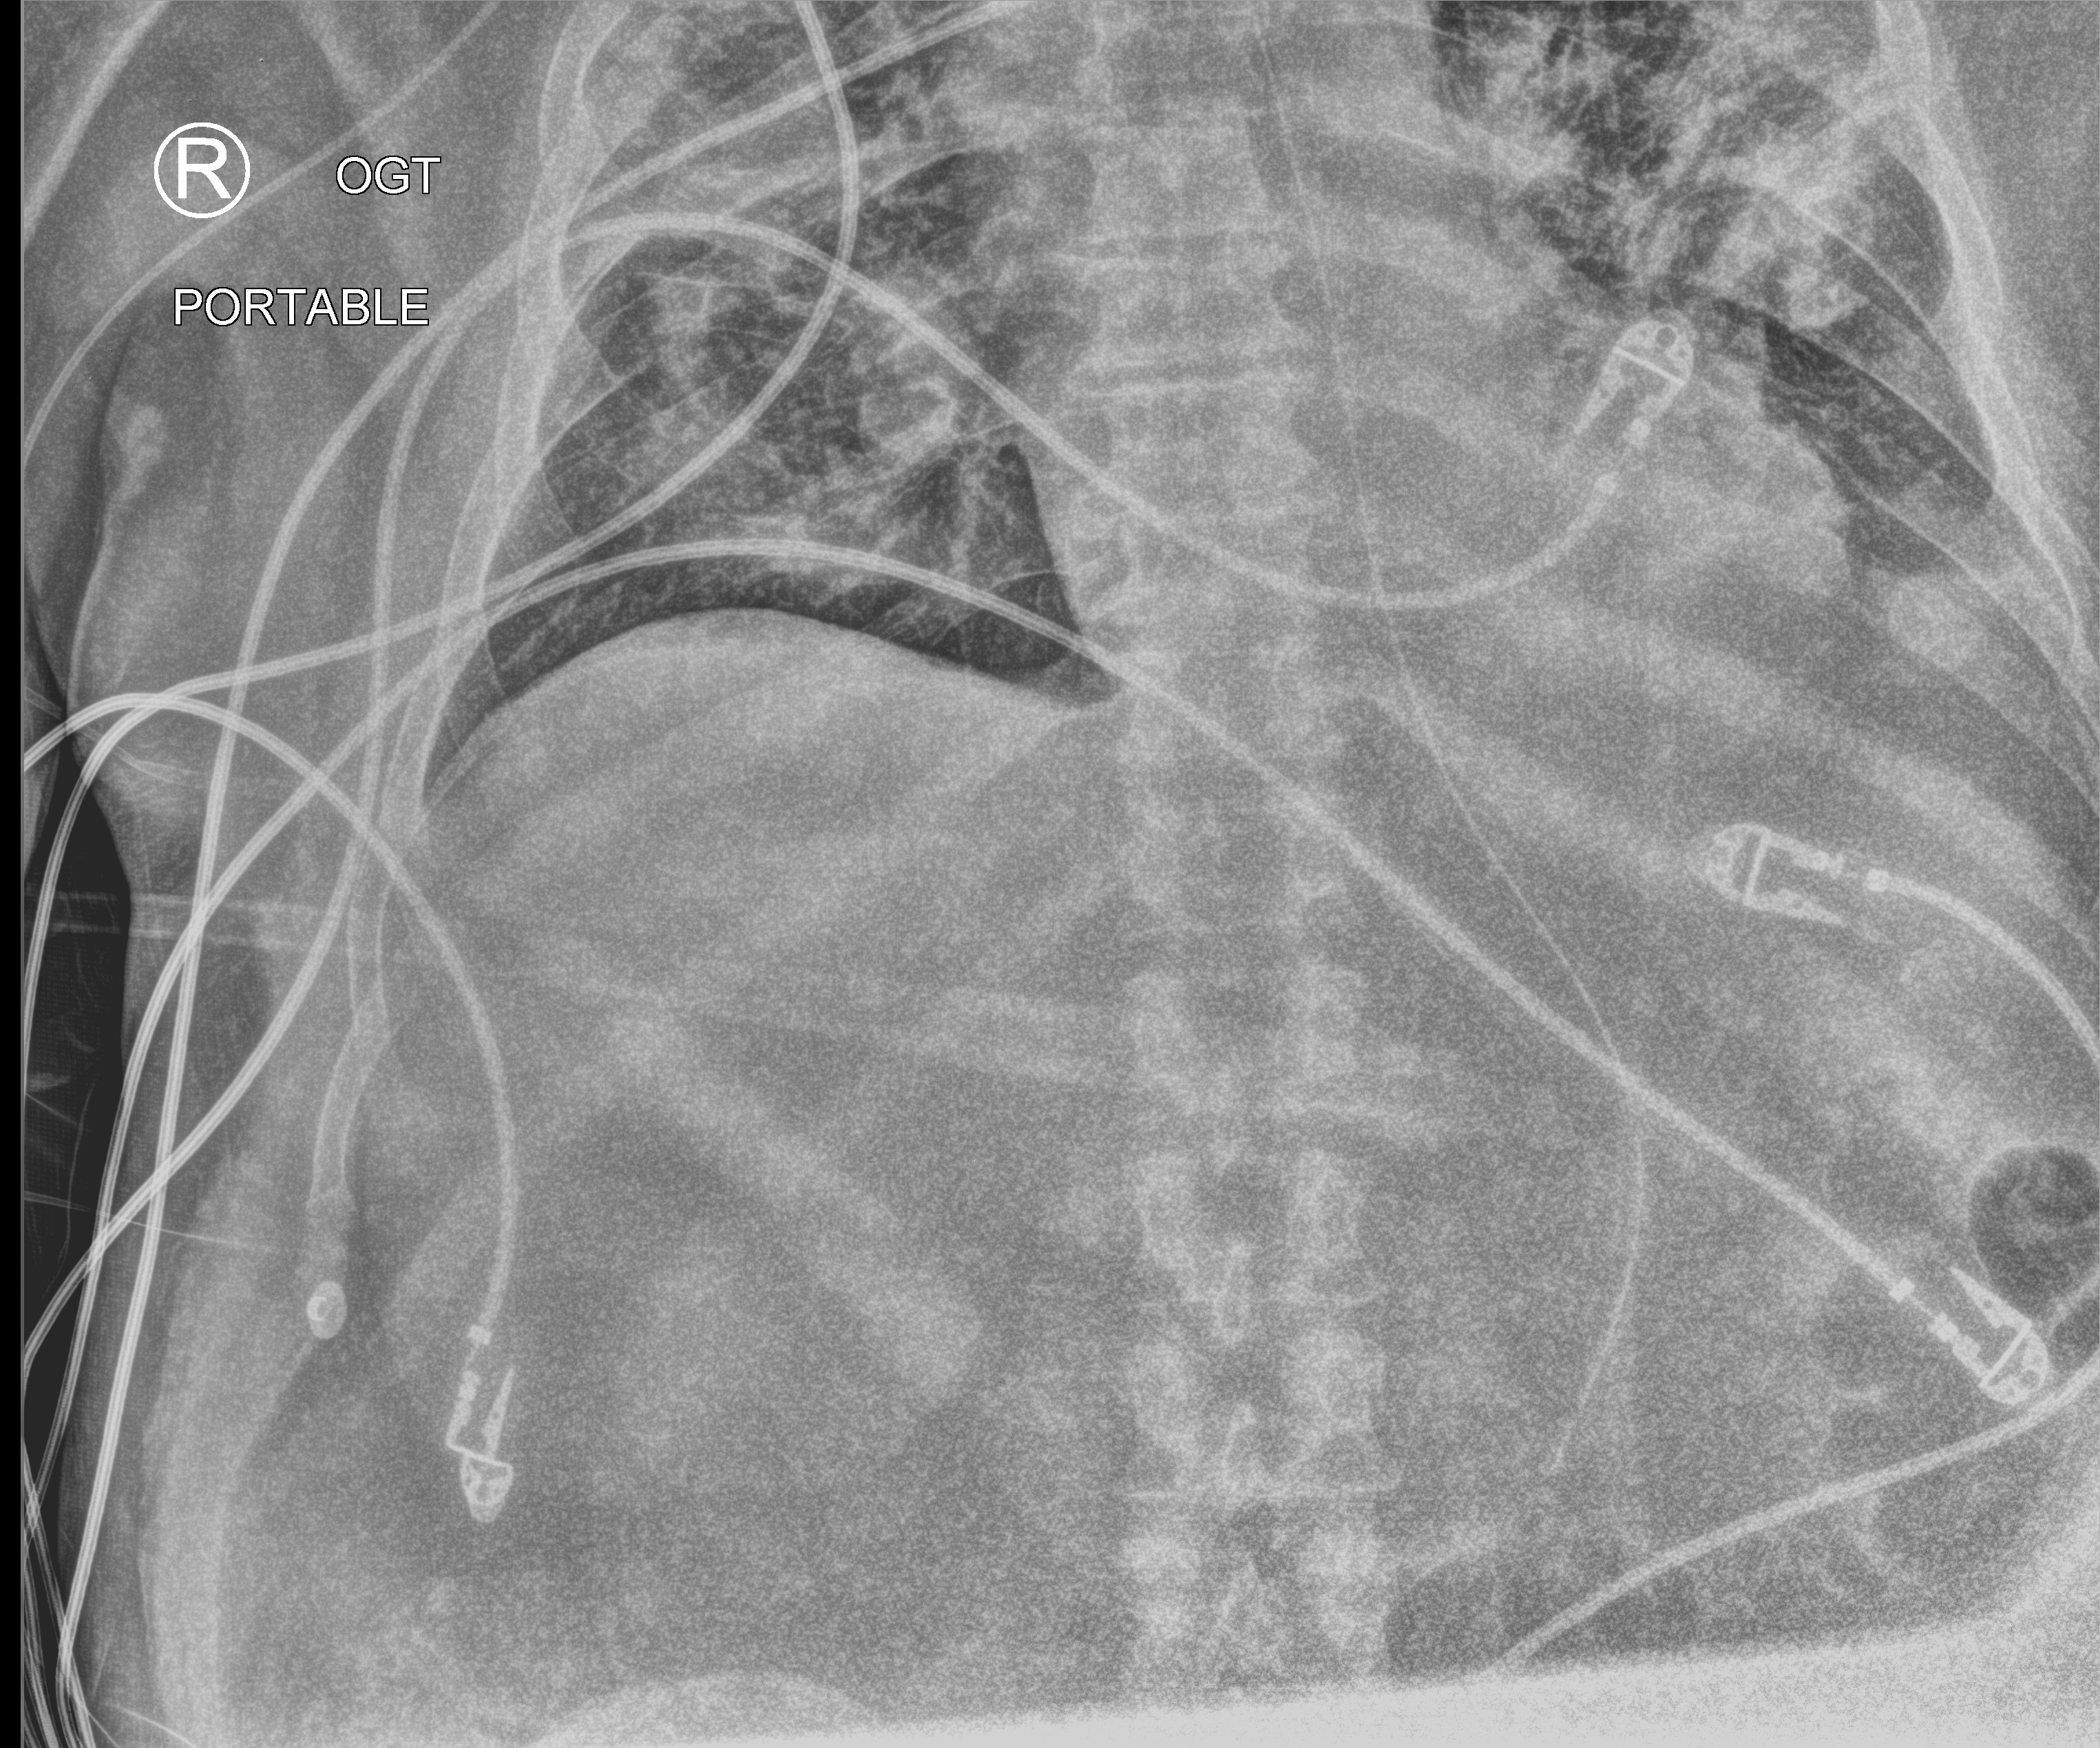
Bedside chest radiograph (computed radiography). Male patient hospitalised with COVID-19, age 60–74 years.
Admission-level facts for this patient (not findings on this image; timing relative to this image not recorded):
- mechanically ventilated during this hospital stay: yes
- chronic kidney disease (admission record): no
- admitted to intensive care during this hospital stay: yes